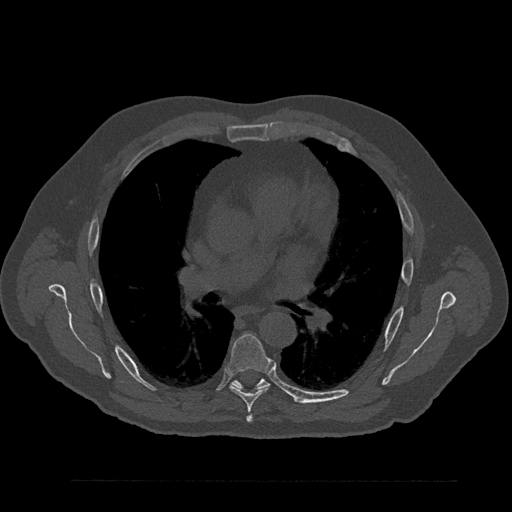
CT including the spine, one axial slice; position 540 of 797 along the scan axis; 120 kVp; bone window (W 1800 / L 400 HU); 0.5 mm slice thickness; 512 × 512 image matrix, field of view 430 × 430 mm. Patient: male, 61 years. From the clinical record (not read from this slice): primary cancer: prostate.
Structures marked on this image (semi-automatically segmented with operator editing):
- T6 vertebra: box from (x=228, y=334) to (x=272, y=422) px
- T7 vertebra: (x=233, y=379)–(x=269, y=389)